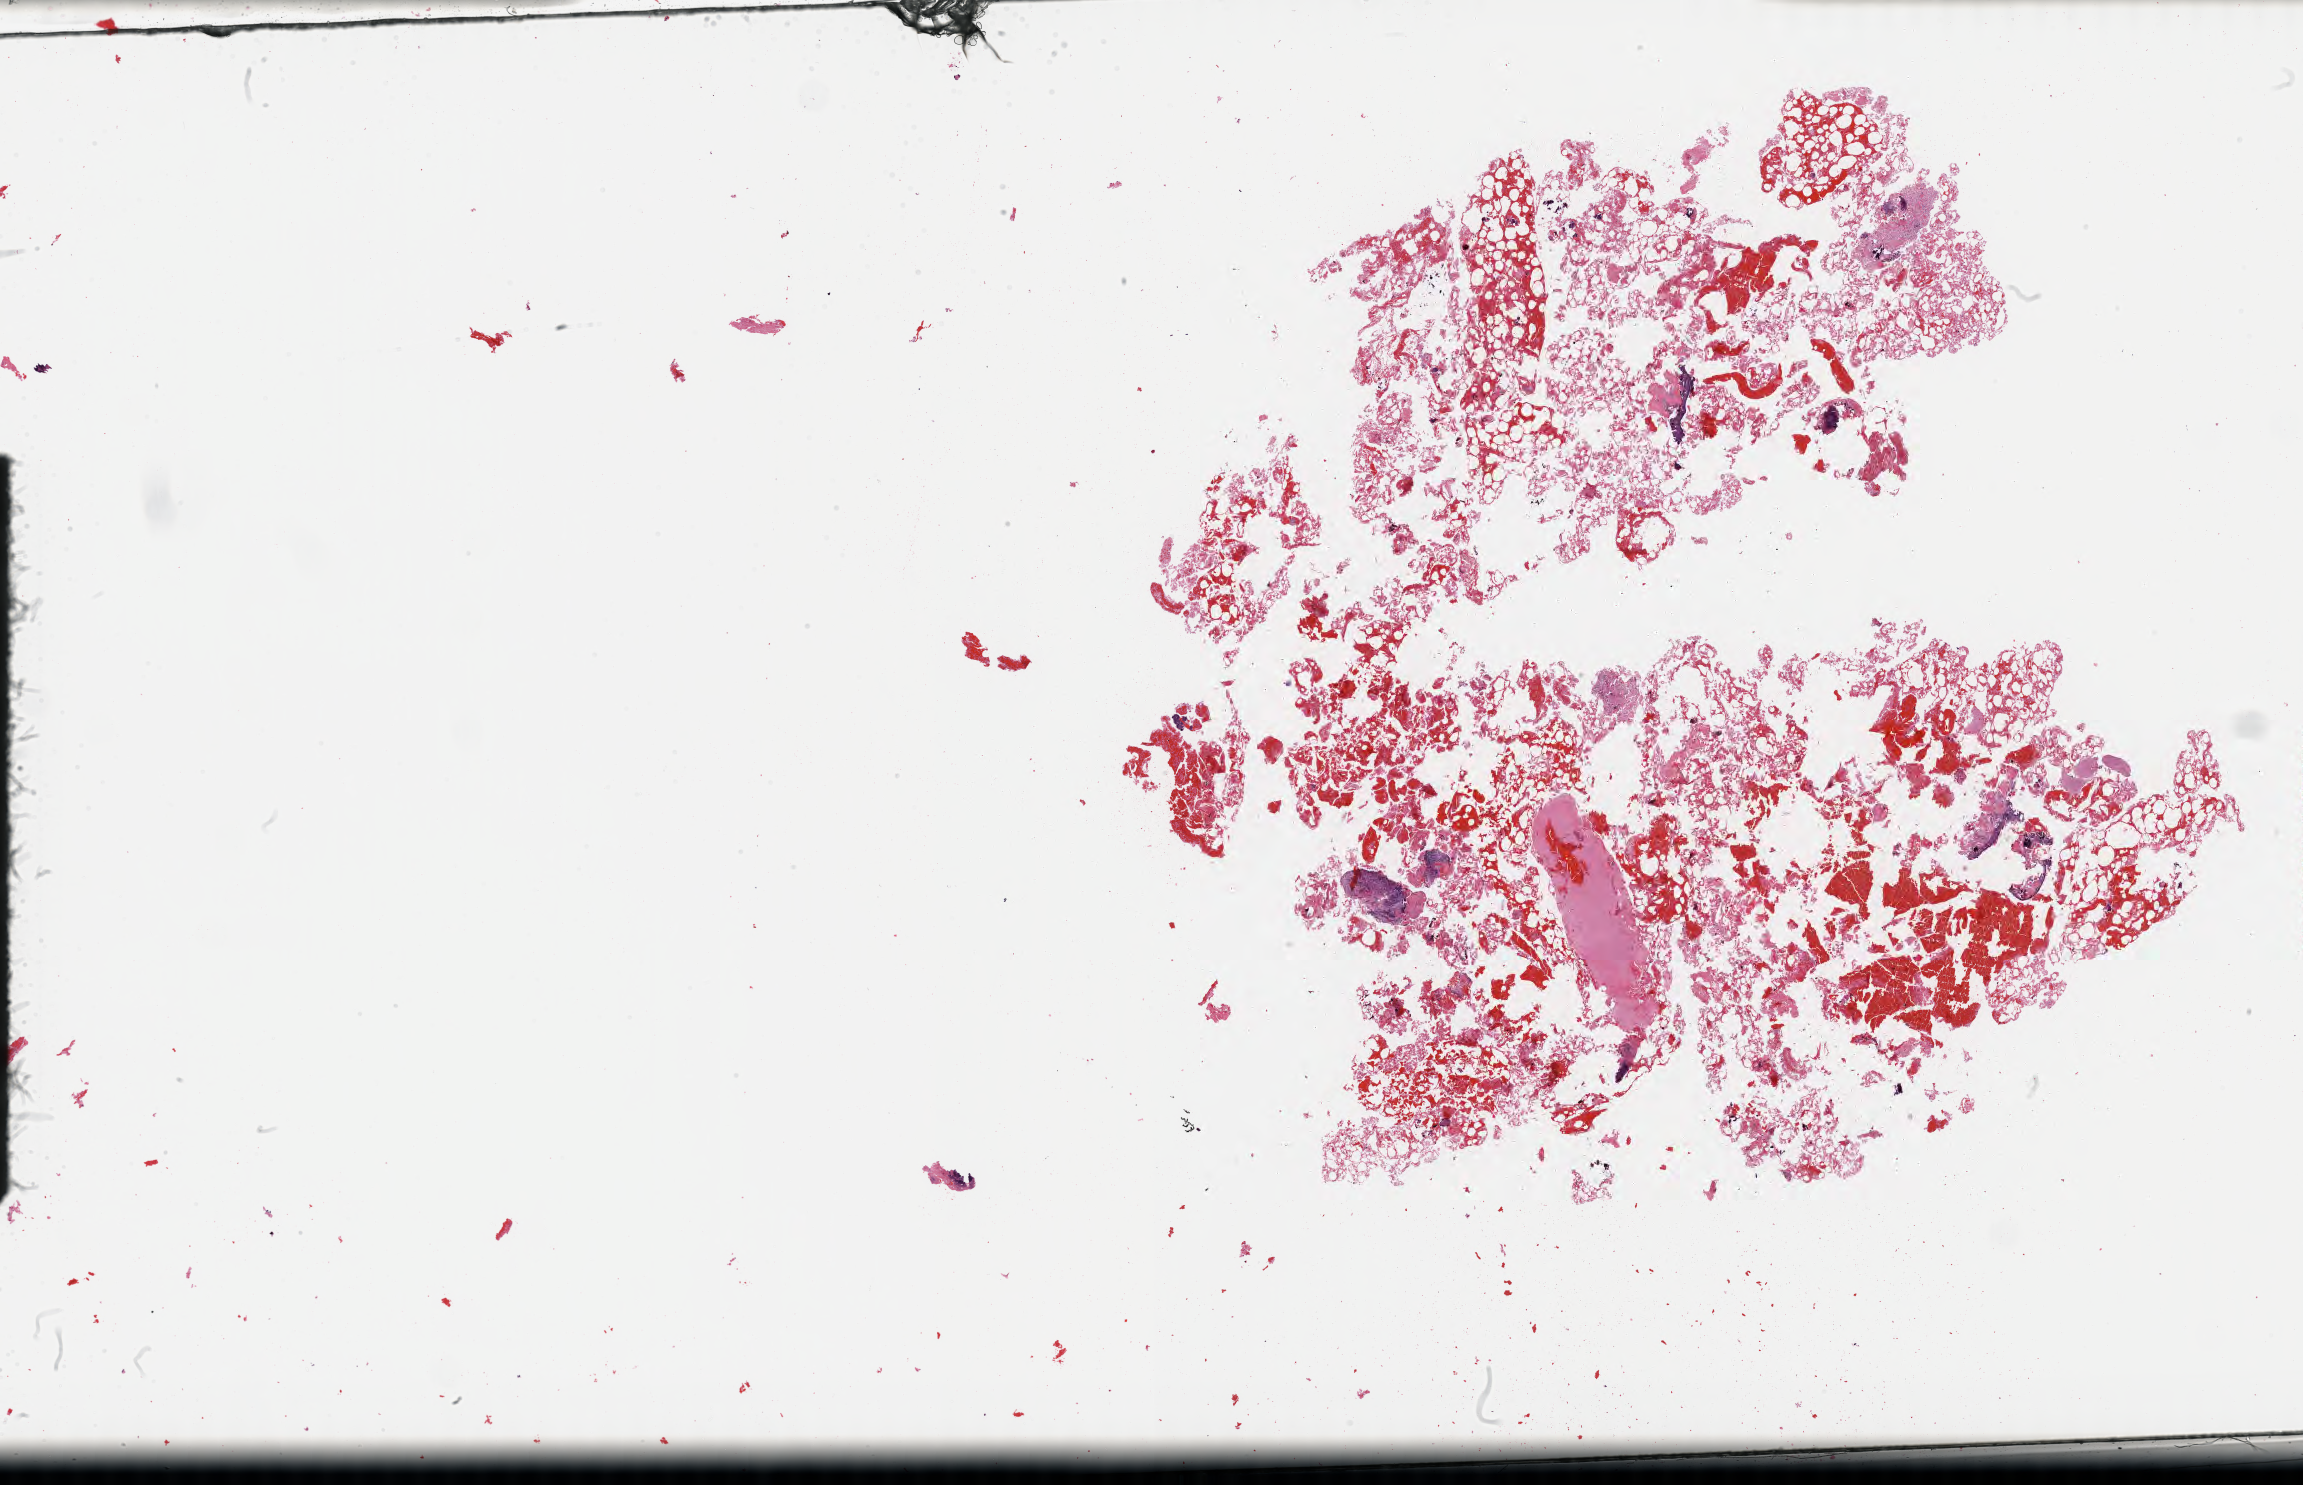
Haematoxylin and eosin whole-slide image of tumor tissue from the brain, a low-resolution overview of the entire scanned area, about 37.2 x 24.0 mm, FFPE section. Female patient, age 37 months (3 years 1 month).
- recorded diagnosis: Craniopharyngioma, adamantinomatous